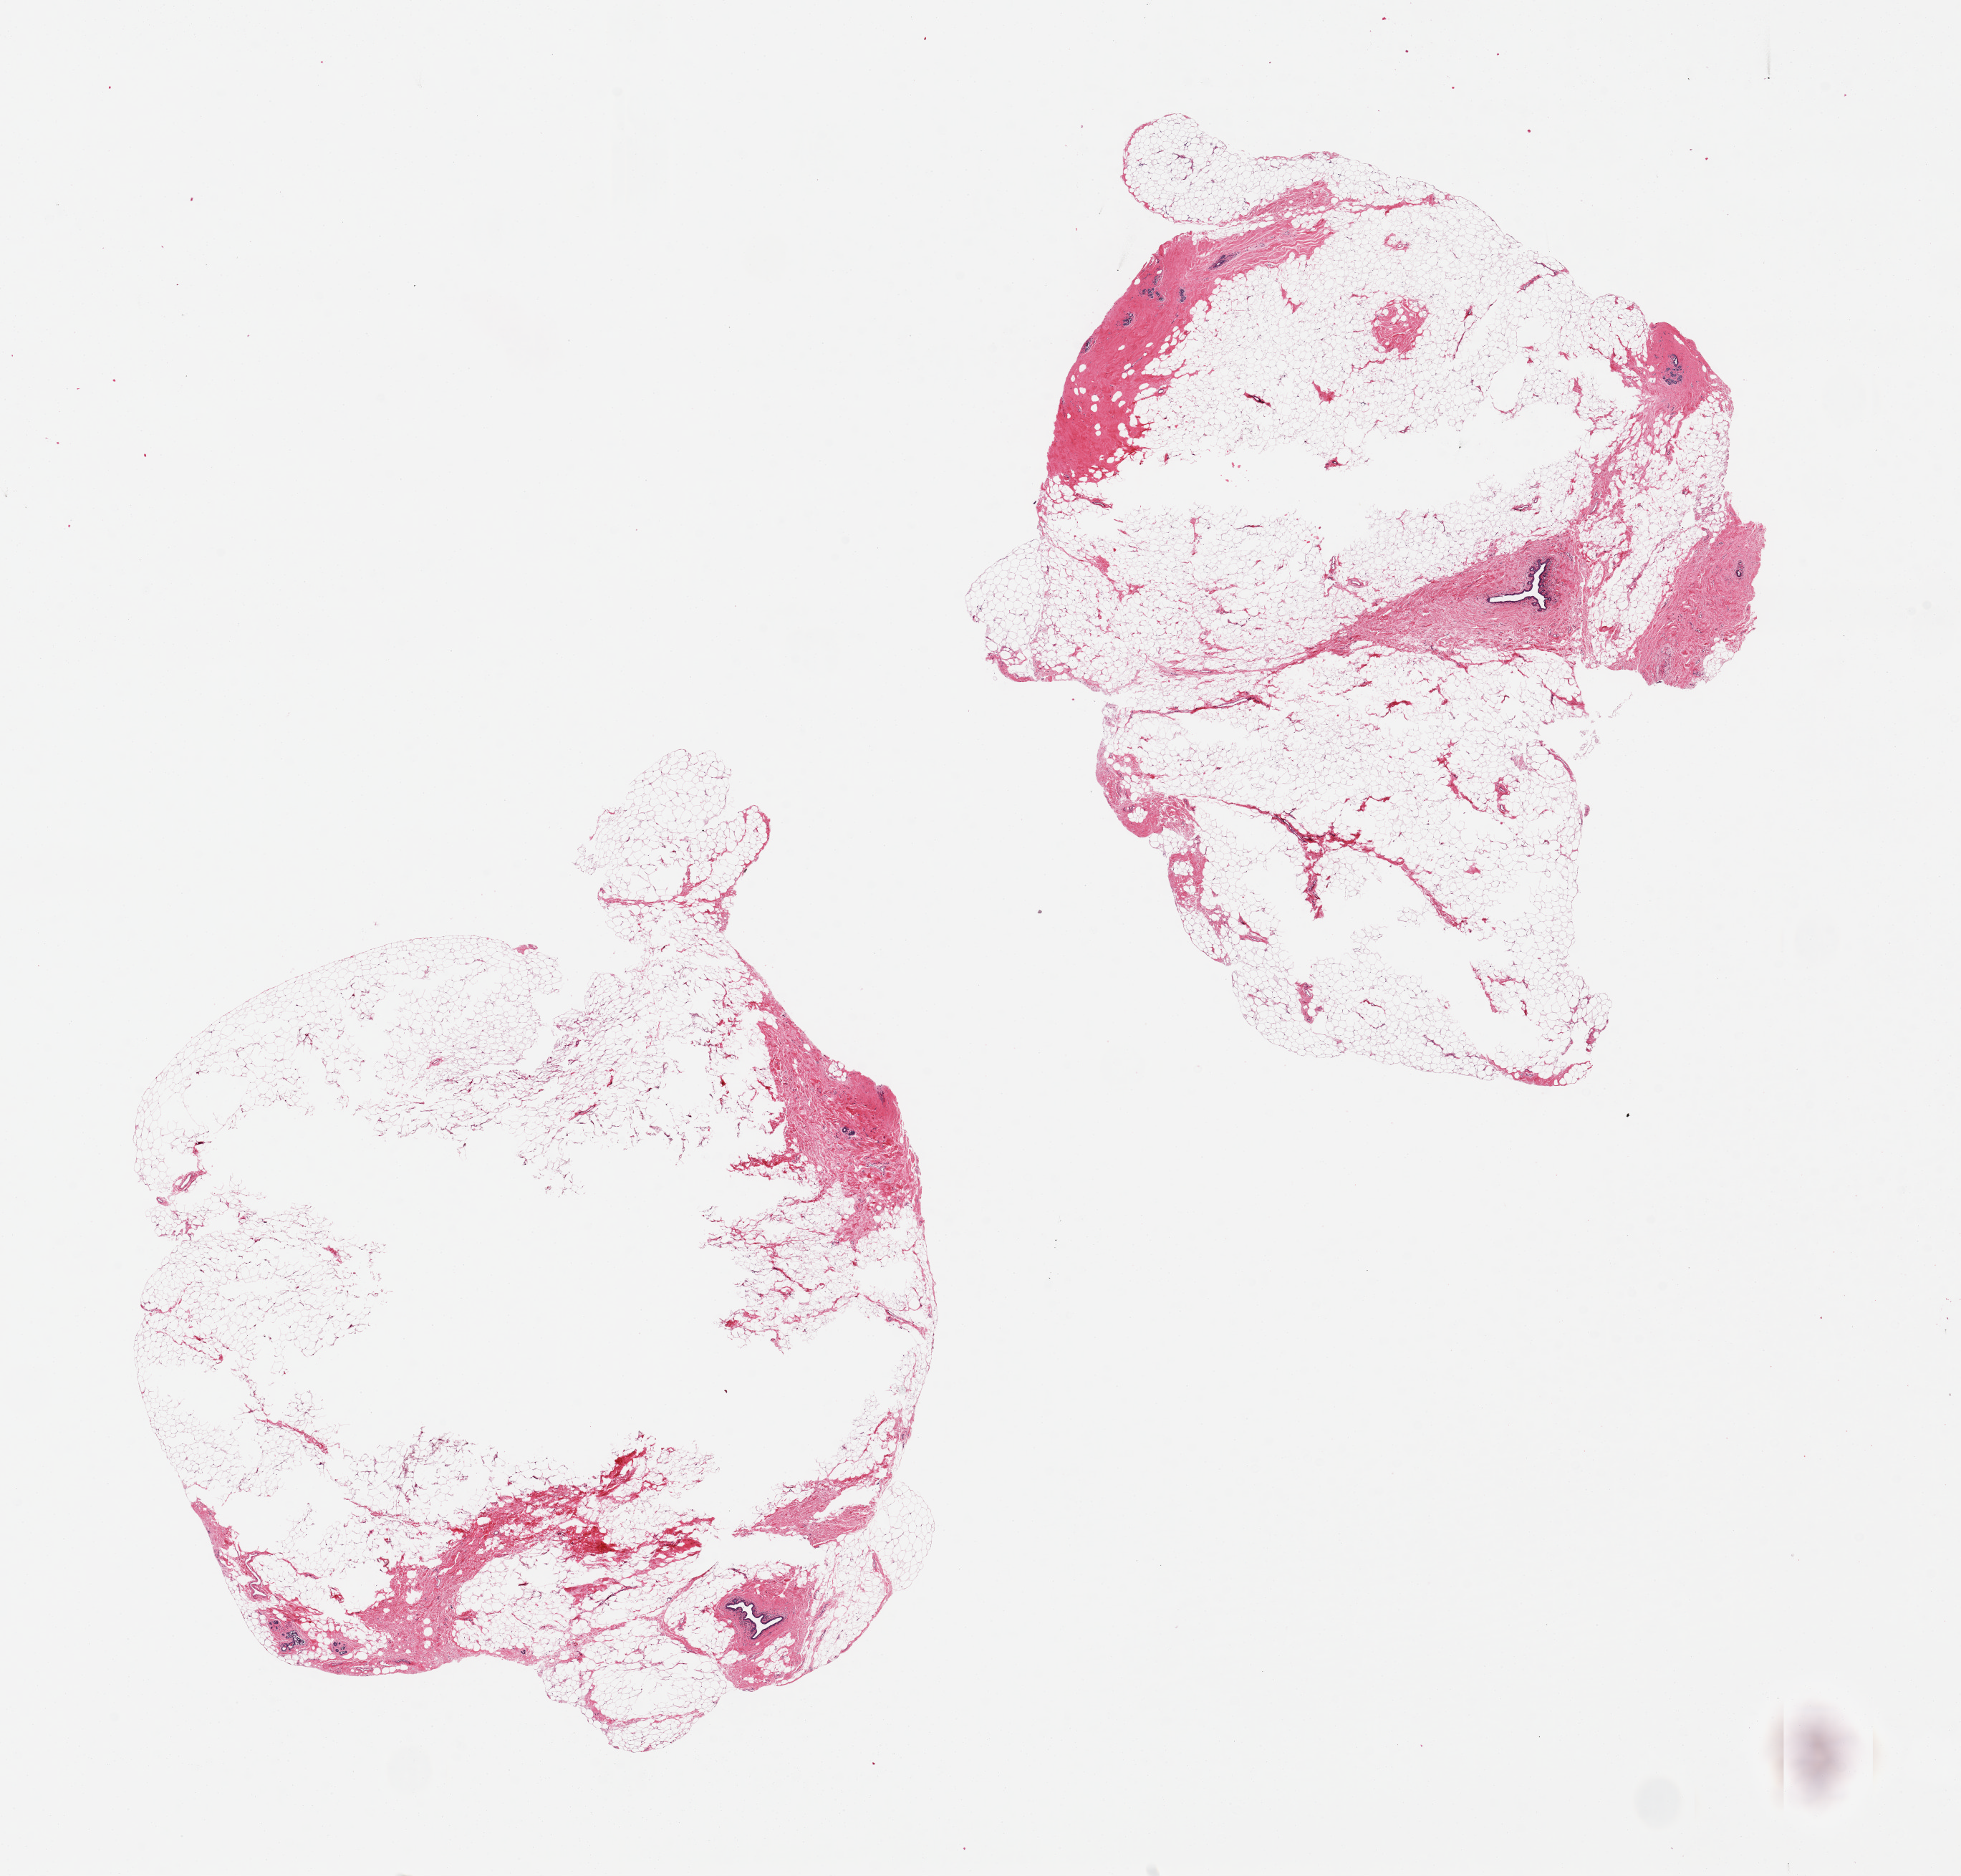
Digitized H&E-stained section — low-resolution overview of the scanned area, about 21.7 x 20.7 mm (from a 20x scan), PAXgene-fixed, paraffin-embedded tissue, target tissue: breast, donor tissue sample. Donor sex: female.
- review note (as recorded): 2 pieces 11x9 & 9x8 mm; atrophic ductal mammary tissue, mostly adipose; largest piece has a central hollow defect